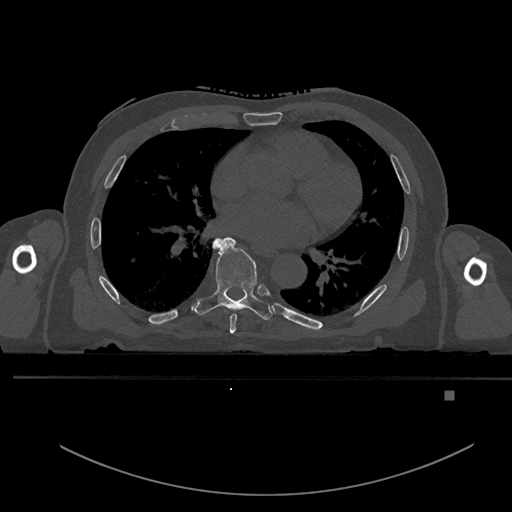
CT including the spine, one axial slice; slice 265 of 969 in the series (ordered by position); bone window (W 1800 / L 400 HU); 0.5 mm slice thickness; 512 × 512 image matrix. Male patient, age 82 years. Case-level facts recorded for this patient, not image findings: primary cancer: prostate; vertebrae with lytic lesions (as recorded): T11, T9, T8, T2.
Structures marked on this image (semi-automatically segmented with operator editing):
- T6 vertebra: bounding box [x1, y1, x2, y2] px = [229, 313, 237, 334]
- T7 vertebra: [192, 237, 273, 320]